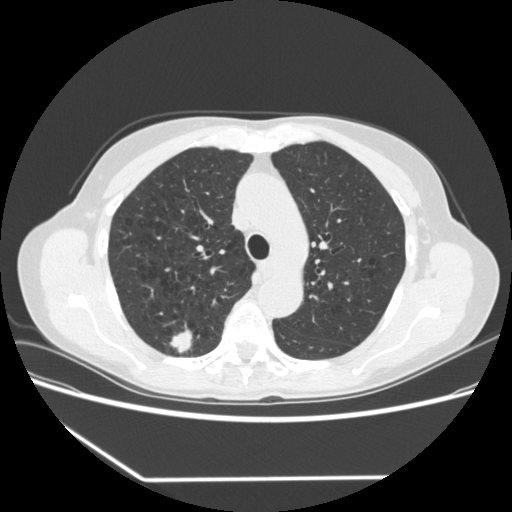
Low-dose screening chest CT, one axial slice; slice 239 of 323 in the series (ordered by position); reconstruction kernel STANDARD; 120 kVp; lung window (W 1500 / L -600 HU); 1.25 mm slice thickness; 512 × 512 image matrix.
Annotated regions visible in this slice (manually delineated by an expert):
- lesion 1 (tumor, upper lobe of right lung): bounding box [x1, y1, x2, y2] px = [170, 325, 192, 354]